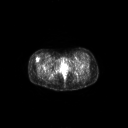
FDG PET of an extremity soft-tissue mass (from a PET/CT study), one axial slice; position 51 of 267 along the scan axis; 3.27 mm slice thickness; 128 × 128 image matrix, field of view 700 × 700 mm. Female patient, age 34 years. Case-level facts recorded for this patient, not image findings: histological type: synovial sarcoma; grade: intermediate; site of the primary tumour: right thigh.
Annotated regions visible in this slice (expert contour drawn on MRI and transferred to this co-registered scan by the dataset authors):
- gross tumour volume including surrounding oedema: bounding box (x1, y1, x2, y2) in pixels: (35, 57, 39, 62)
- gross tumour volume (mass): (35, 57, 39, 62)